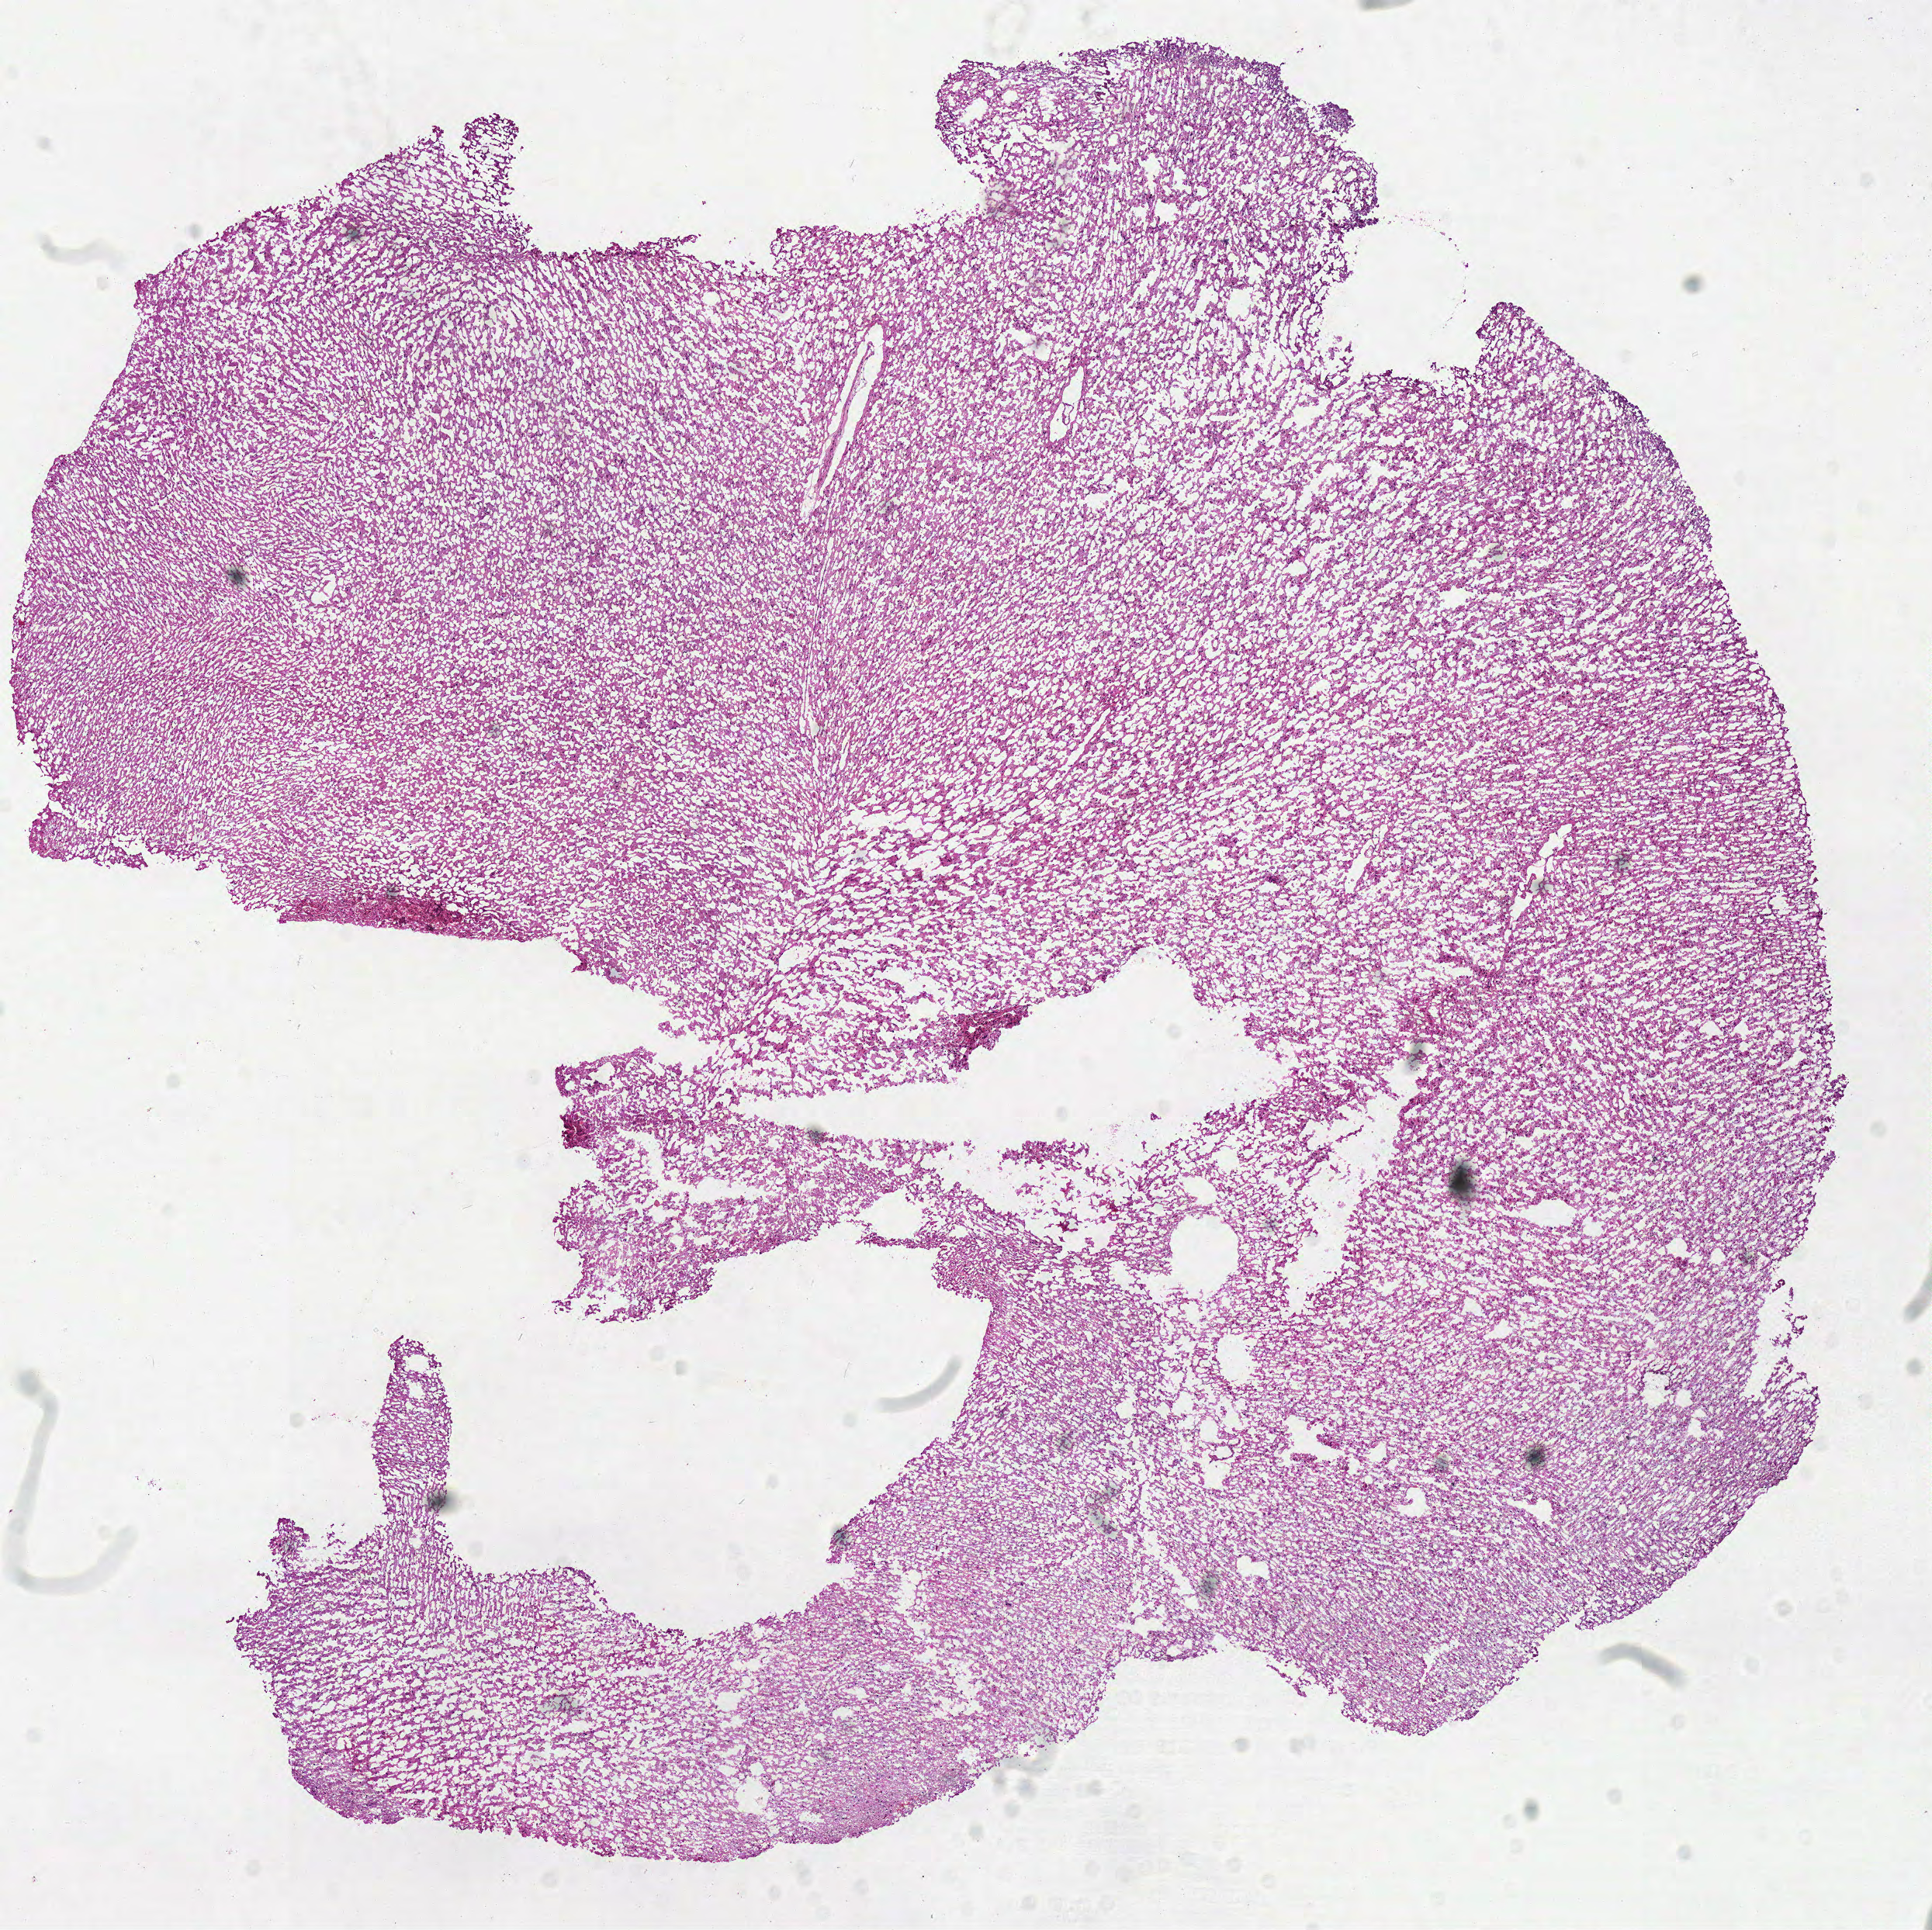
Hematoxylin and eosin (H&E) stained whole-slide image — shown as a low-resolution overview of the whole scanned area (about 9.8 x 9.8 mm, slide scanned at 40x); frozen section from the top of the tissue portion; primary tumour sample from the brain. Male, age 30 years at initial diagnosis. Histologic grade: G2 (moderately differentiated). Slide review estimates, as recorded: tumour cells 100%, tumour nuclei 70%, normal cells 0%, stromal cells 0%, necrosis 0%.
Pathologic diagnosis: Astrocytoma, NOS.